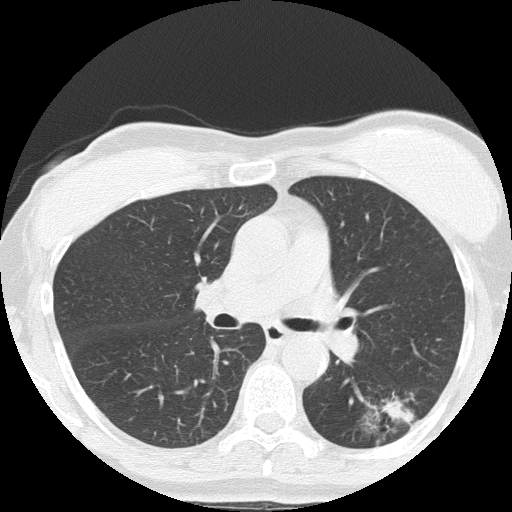
Low-dose screening chest CT, axial slice, third screening round (two years after baseline), lung window (W 1500 / L -600 HU), slice 63 of 152 in the series. Female participant, aged 64 years at enrolment. Former smoker at enrolment.
Lesion marked by an expert reader, bounding box (x1, y1, x2, y2) in pixels: (355, 377, 443, 449). The screening reader recorded 3 non-calcified nodules or masses ≥4 mm on this exam (right upper lobe, left lower lobe, right middle lobe); which of them this box marks is not recorded. Later outcome: lung cancer diagnosed 212 days after this screen — adenocarcinoma, NOS, left lower lobe, moderately differentiated (G2), stage IA (AJCC 6th edition), 17 mm at pathology.